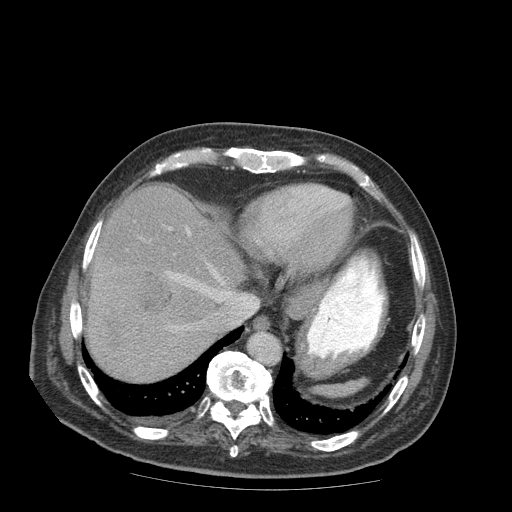
Contrast-enhanced abdominal CT (liver protocol), one axial slice. Slice 74 of 99 in the series (ordered by position). Reconstruction kernel STANDARD. 140 kVp. Soft-tissue window (W 400 / L 40 HU). 512 × 512 image matrix, field of view 420 × 420 mm. From the clinical record (not read from this slice): diagnosis: hepatocellular carcinoma (patient treated with transarterial chemoembolisation; whether this scan precedes or follows treatment is not stated here); TNM stage (as recorded): Stage-IIIB; Child-Pugh class: A; tumour differentiation: well differentiated.
Annotated regions visible in this slice (semi-automatically segmented with operator editing):
- liver parenchyma outside the tumour (the mass and vessels are separate outlines, so this box may not span the whole liver): bounding box <88,184,244,380> (left, top, right, bottom; pixels)
- mass: <87,258,175,326>
- liver vessels: <166,228,225,332>